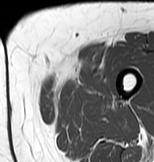
MRI of an extremity soft-tissue mass, one axial slice; slice 10 of 83 in the series (ordered by position); MR volume resampled by the dataset authors to the PET/CT grid (not the native acquisition matrix); 3.27 mm slice thickness; 154 × 162 image matrix, field of view 150 × 158 mm. Female patient. Case-level facts recorded for this patient, not image findings: histological type: myxofibrosarcoma; grade: intermediate; site of the primary tumour: left thigh.
Structures marked on this image (expert contour drawn on MRI and transferred to this co-registered scan by the dataset authors):
- gross tumour volume including surrounding oedema: bounding box [x1, y1, x2, y2] px = [42, 64, 113, 104]